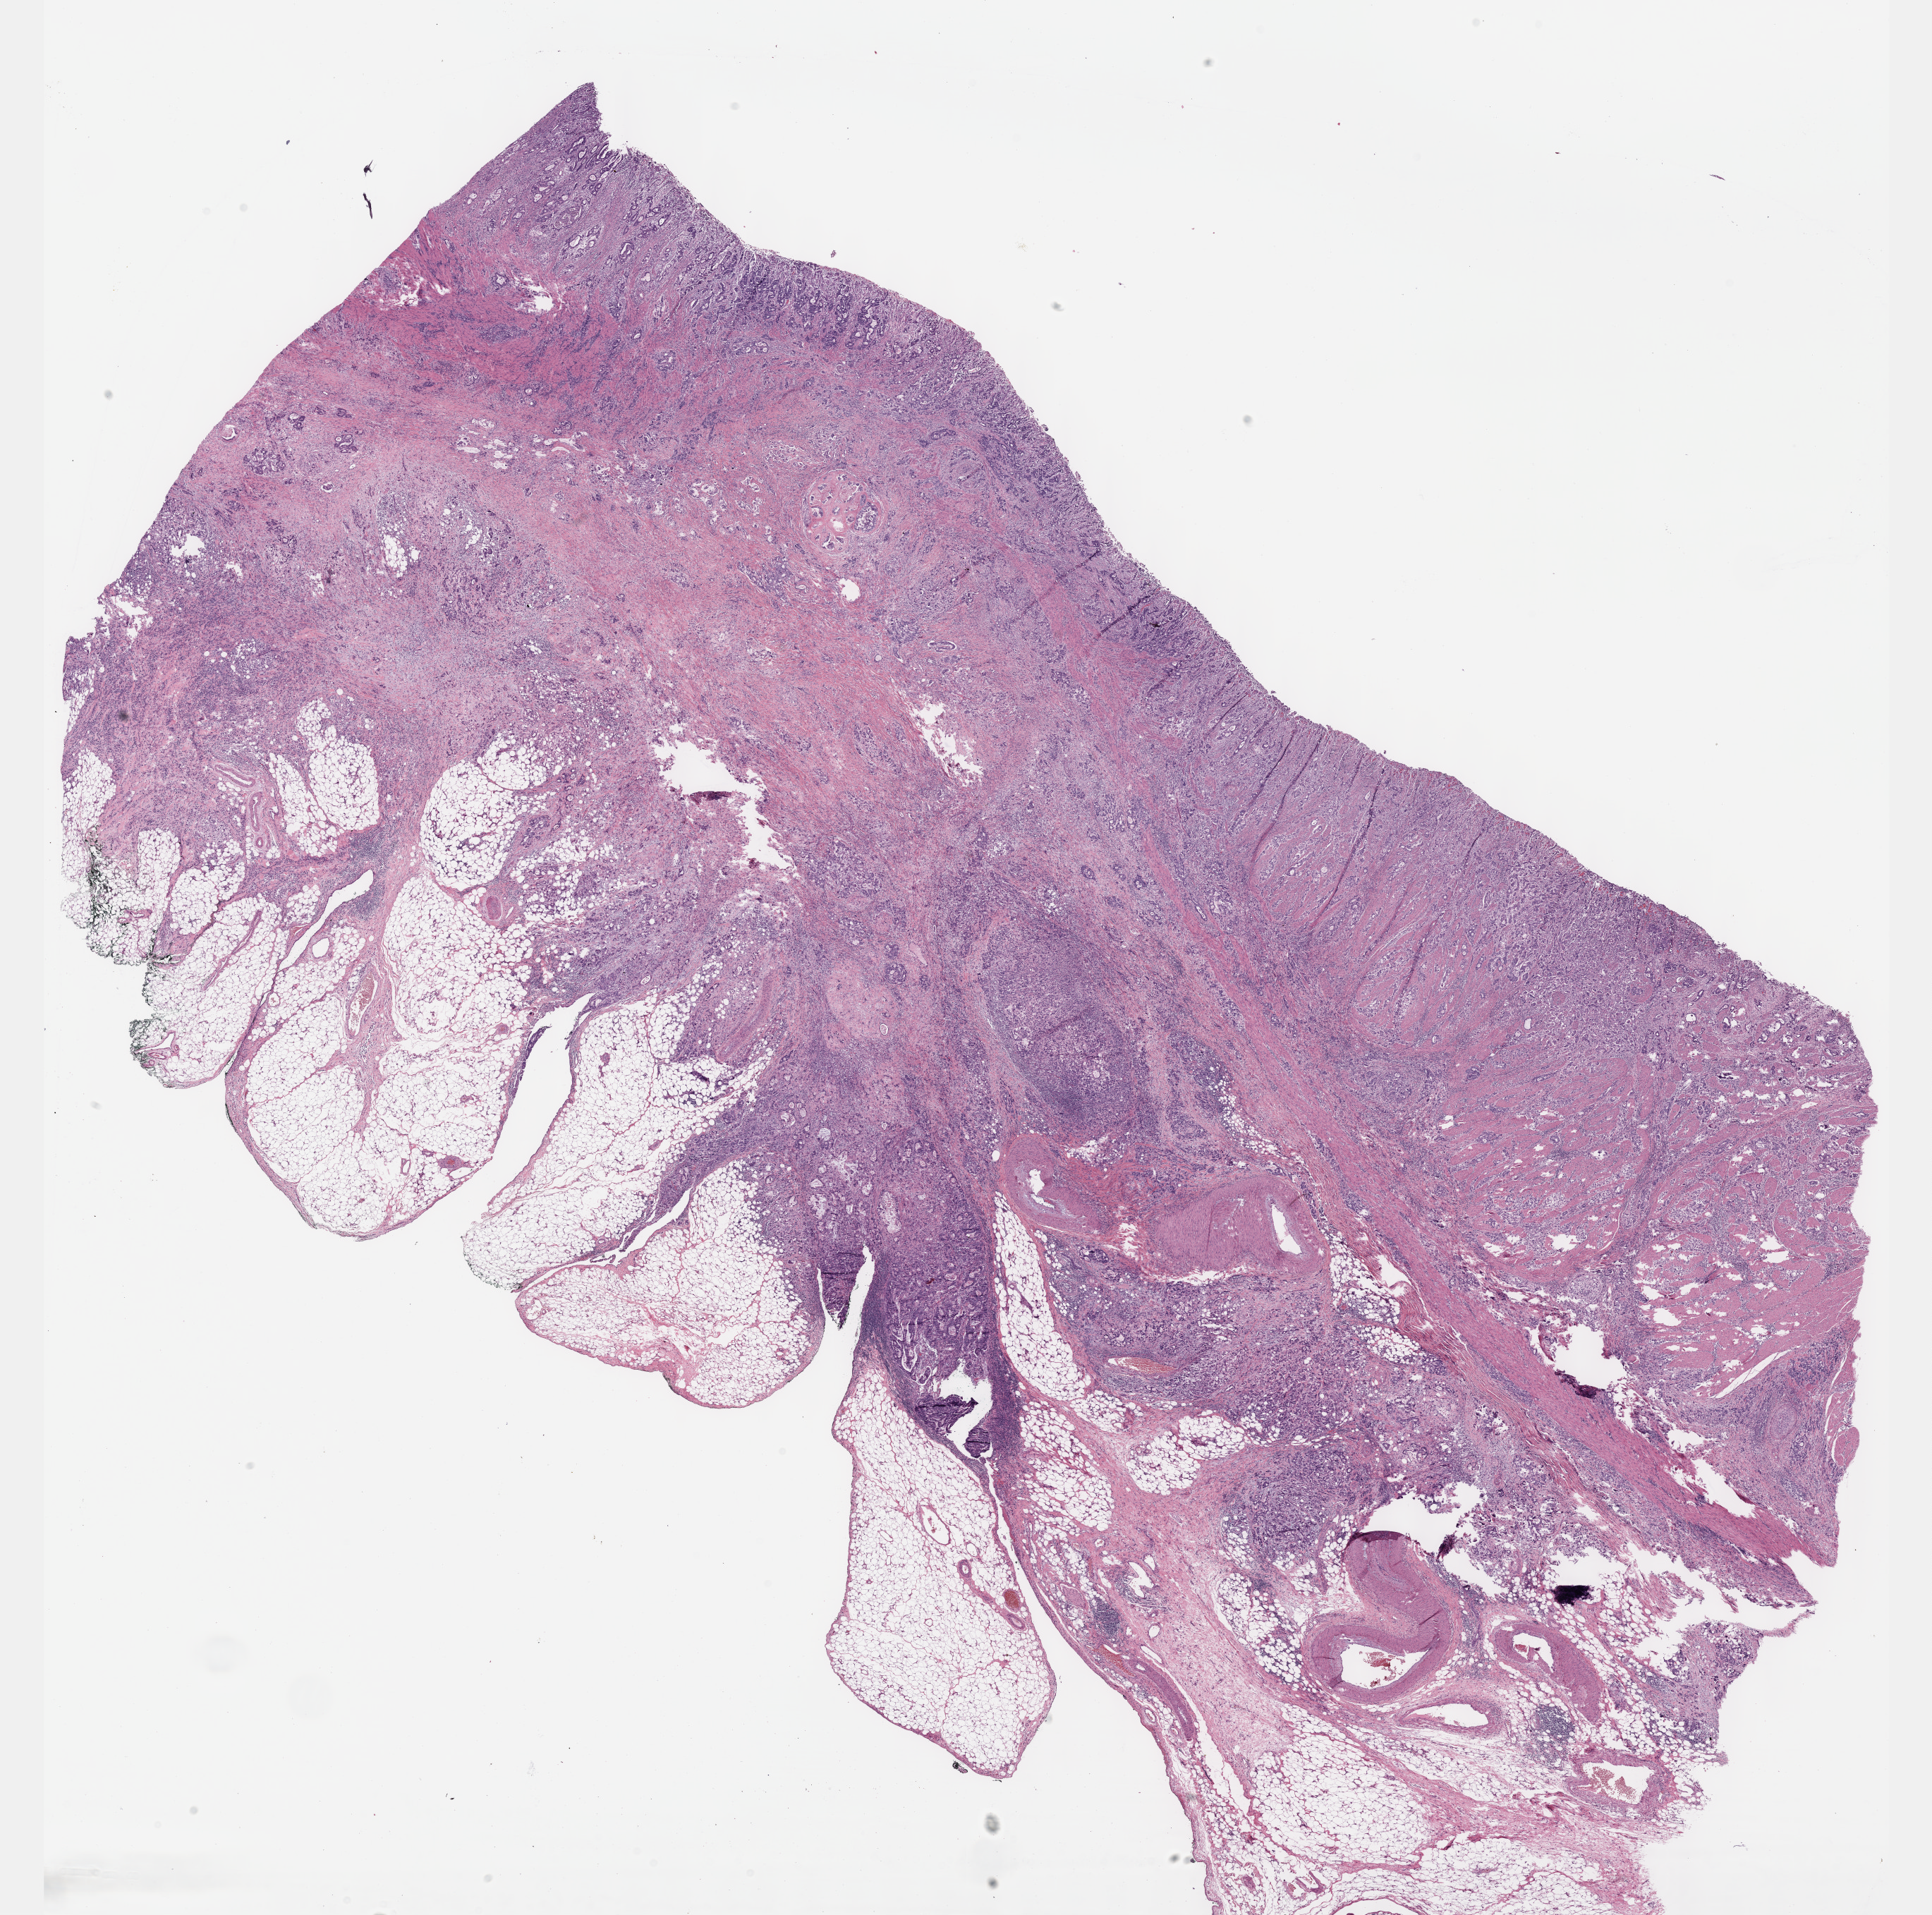
Whole-slide histology image, H&E, whole scanned area (about 22.1 x 21.9 mm, slide scanned at 40x) shown as a low-resolution overview, formalin-fixed paraffin-embedded (FFPE) diagnostic section, sample: primary tumour, stomach. Male, age 67 years at initial diagnosis. Histologic grade: G3 (poorly differentiated).
Pathologic diagnosis: Tubular adenocarcinoma (gastric antrum). Lymph nodes positive (case pathology): 50 of 60 examined. AJCC pathologic stage: IIIC (6th edition).